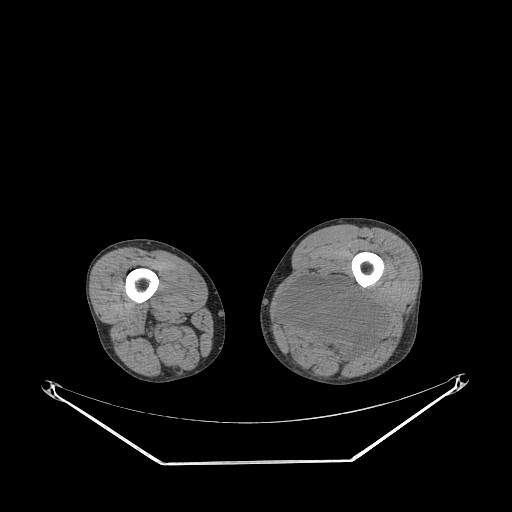
CT of an extremity soft-tissue mass (from a PET/CT study), one axial slice. 140 kVp. Soft-tissue window (W 400 / L 40 HU). 3.75 mm slice thickness. 512 × 512 image matrix, field of view 500 × 500 mm. Male patient. Case-level facts recorded for this patient, not image findings: histological type: undifferentiated pleomorphic liposarcoma; grade: high; site of the primary tumour: left thigh.
Annotated regions visible in this slice (expert contour drawn on MRI and transferred to this co-registered scan by the dataset authors):
- gross tumour volume including surrounding oedema: bounding box <281,278,385,359> (left, top, right, bottom; pixels)
- gross tumour volume (mass): <281,278,385,359>